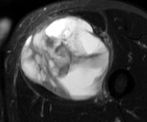
MRI of an extremity soft-tissue mass, one axial slice; position 33 of 52 along the scan axis; T2-weighted fat-saturated; MR volume resampled by the dataset authors to the PET/CT grid (not the native acquisition matrix); 3.27 mm slice thickness; 147 × 122 image matrix, field of view 144 × 119 mm. Male patient. From the clinical record (not read from this slice): histological type: pleiomorphic liposarcoma; grade: high; site of the primary tumour: left thigh.
Outlined on this slice (expert contour drawn on MRI and transferred to this co-registered scan by the dataset authors):
- gross tumour volume including surrounding oedema: bounding box (x1, y1, x2, y2) in pixels: (21, 16, 113, 99)
- gross tumour volume (mass): (21, 16, 110, 99)